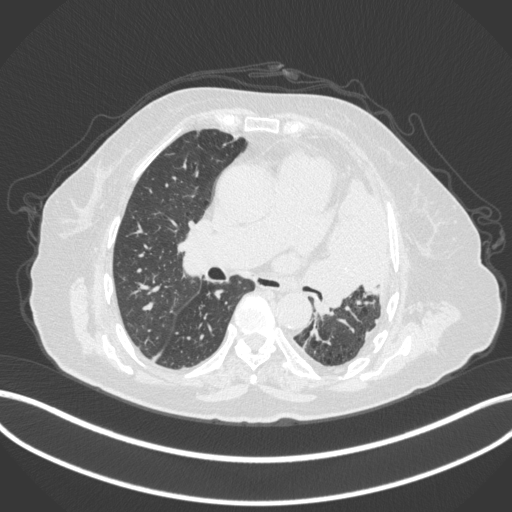
Chest CT, one axial slice; slice 208 of 399 in the series (ordered by position); reconstruction kernel B31f; lung window (W 1500 / L -600 HU); 1 mm slice thickness; 512 × 512 image matrix, field of view 400 × 400 mm. Female patient, age 75 years. Case-level facts recorded for this patient, not image findings: clinical TNM (as recorded): T3 N3 M1.
Annotated regions visible in this slice (rectangle marked by the reading radiologist):
- lung tumour (recorded histology: adenocarcinoma): bounding box [x1, y1, x2, y2] px = [308, 171, 392, 316]